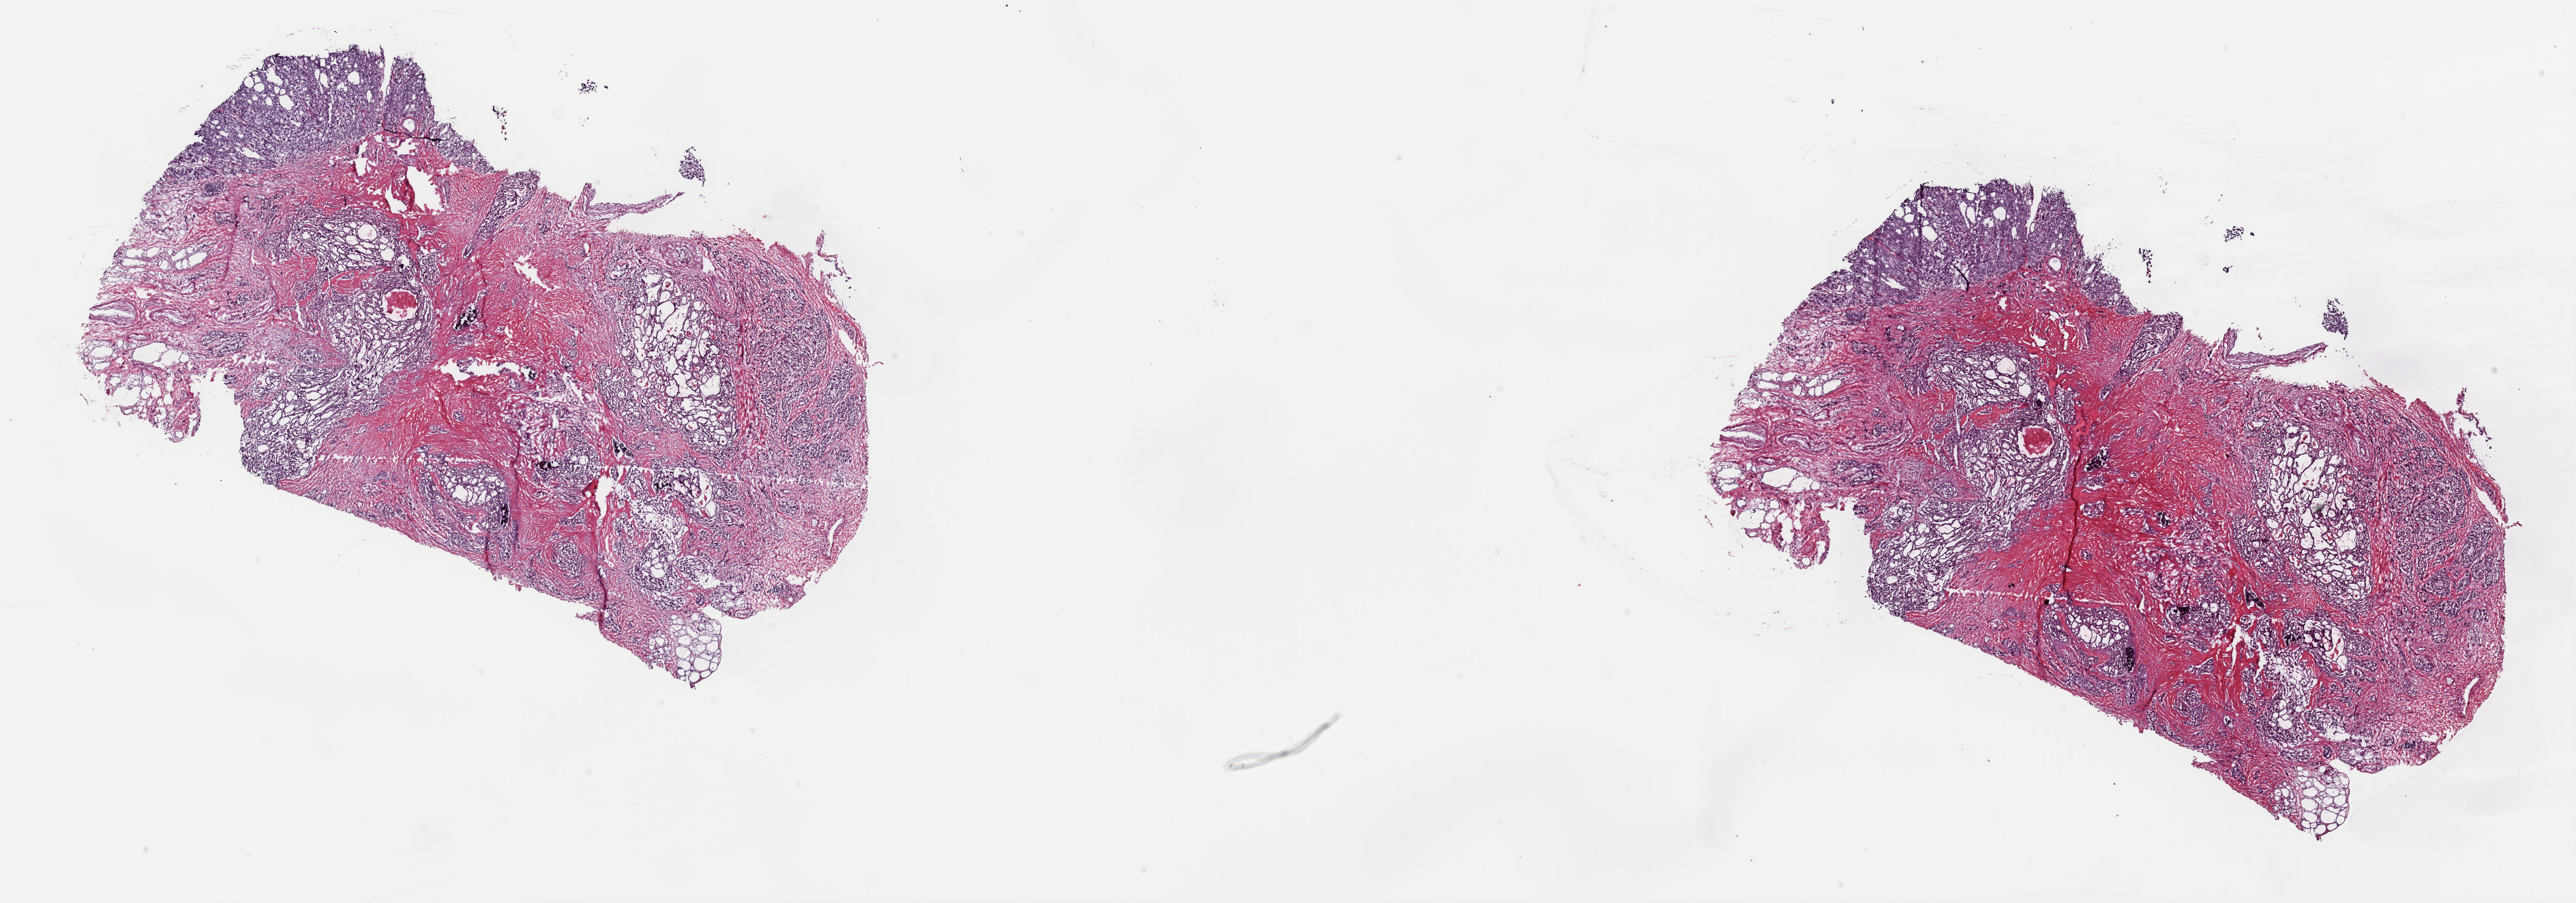
Digitized Hematoxylin and eosin (H&E) stained tissue section (whole slide), whole scanned area (about 29.8 x 10.5 mm, from a 40x scan) shown as a low-resolution overview. Frozen section from the top of the tissue portion. Primary tumour sample from the thyroid. Female, age 60 years at initial diagnosis. Composition of this section per pathologist review: tumour cells 70%, tumour nuclei 70%.
Pathologic diagnosis: Papillary carcinoma, columnar cell (thyroid gland).